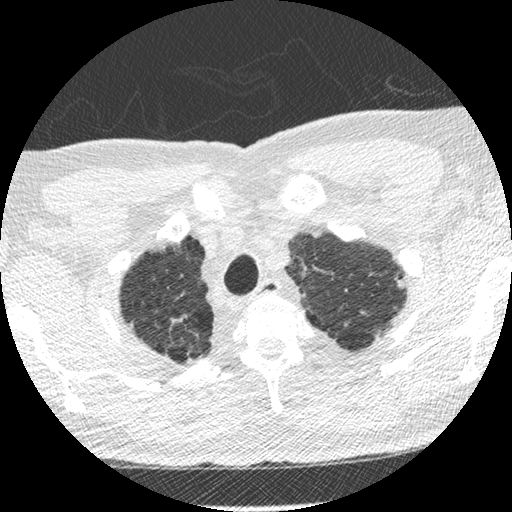
Low-dose screening chest CT, one axial slice. Reconstruction kernel STANDARD. 120 kVp. Lung window (W 1500 / L -600 HU). 1.25 mm slice thickness. 512 × 512 image matrix, field of view 330 × 330 mm.
Outlined on this slice (manually delineated by an expert):
- lesion 1 (tumor, upper lobe of left lung): box from (x=395, y=277) to (x=404, y=289) px